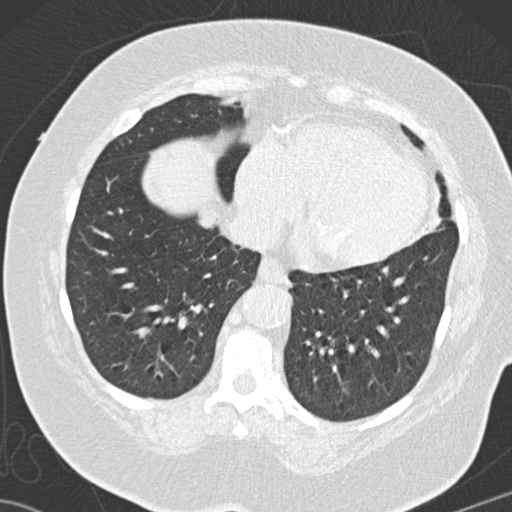
Low-dose screening chest CT, one axial slice; position 45 of 146 along the scan axis; 120 kVp; lung window (W 1500 / L -600 HU); 2 mm slice thickness; 512 × 512 image matrix, field of view 350 × 350 mm.
Outlined on this slice (outlined manually by an expert reader):
- lesion 3 (tumor, lower lobe of right lung): bounding box (x1, y1, x2, y2) in pixels: (197, 206, 219, 229)